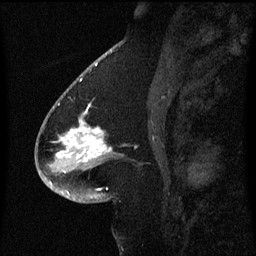
Breast MRI (dynamic contrast-enhanced), one sagittal slice; dynamic contrast-enhanced series, image 2 of 3 at this slice position (ordered by acquisition); 1.5 T; TE 4.2 ms, TR 8.4 ms; 2 mm slice thickness; 256 × 256 image matrix. Patient: female, 54 years. Case-level facts recorded for this patient, not image findings: setting: breast cancer imaged before/during neoadjuvant chemotherapy; receptor status: HR-positive, HER2-negative.
Outlined on this slice (semi-automatic segmentation, software-assisted and operator-edited):
- analysis volume of interest (the breast-tissue region the enhancement analysis was run in; not a lesion): bounding box <46,100,120,171> (left, top, right, bottom; pixels)
- tumour enhancement mask (voxels above the 70 % enhancement threshold inside the analysis volume of interest): <58,106,103,159>